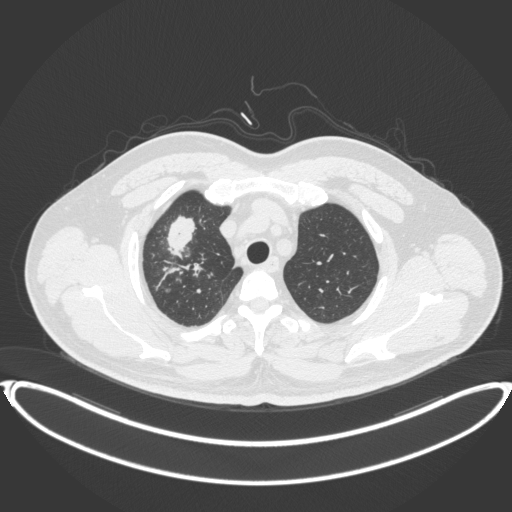
Chest CT, one axial slice. Position 321 of 399 along the scan axis. Lung window (W 1500 / L -600 HU). 1 mm slice thickness. 512 × 512 image matrix. Patient: male, 53 years. From the clinical record (not read from this slice): clinical TNM (as recorded): T2a N0 M0.
Outlined on this slice (rectangle marked by the reading radiologist):
- lung tumour (recorded histology: adenocarcinoma): bounding box (x1, y1, x2, y2) in pixels: (164, 214, 201, 263)